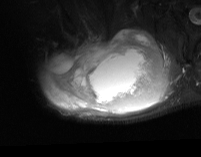
MRI of an extremity soft-tissue mass, one axial slice; slice 48 of 74 in the series (ordered by position); STIR; MR volume resampled by the dataset authors to the PET/CT grid (not the native acquisition matrix); 201 × 157 image matrix. Male patient. Case-level facts recorded for this patient, not image findings: histological type: pleiomorphic spindle cell undifferentiated; grade: high; site of the primary tumour: right parascapusular.
Structures marked on this image (expert contour drawn on MRI and transferred to this co-registered scan by the dataset authors):
- gross tumour volume including surrounding oedema: bounding box [x1, y1, x2, y2] px = [42, 27, 182, 117]
- gross tumour volume (mass): [46, 29, 166, 113]